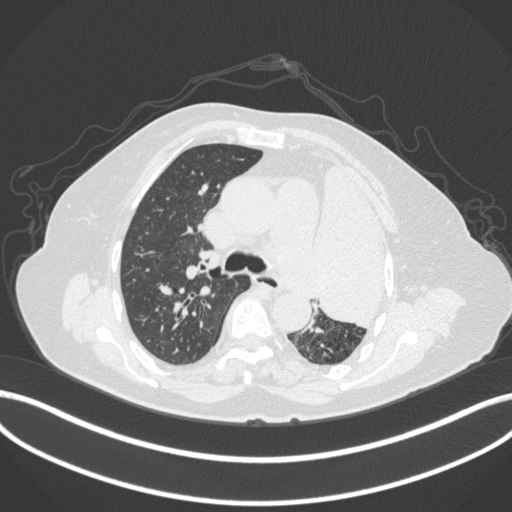
Chest CT, one axial slice. Position 255 of 399 along the scan axis. Reconstruction kernel B31f. 120 kVp. Lung window (W 1500 / L -600 HU). 1 mm slice thickness. 512 × 512 image matrix, field of view 400 × 400 mm. Patient: female, 75 years. Case-level facts recorded for this patient, not image findings: clinical TNM (as recorded): T3 N3 M1.
Structures marked on this image (rectangle marked by the reading radiologist):
- lung tumour (recorded histology: adenocarcinoma): box from (x=300, y=153) to (x=394, y=336) px